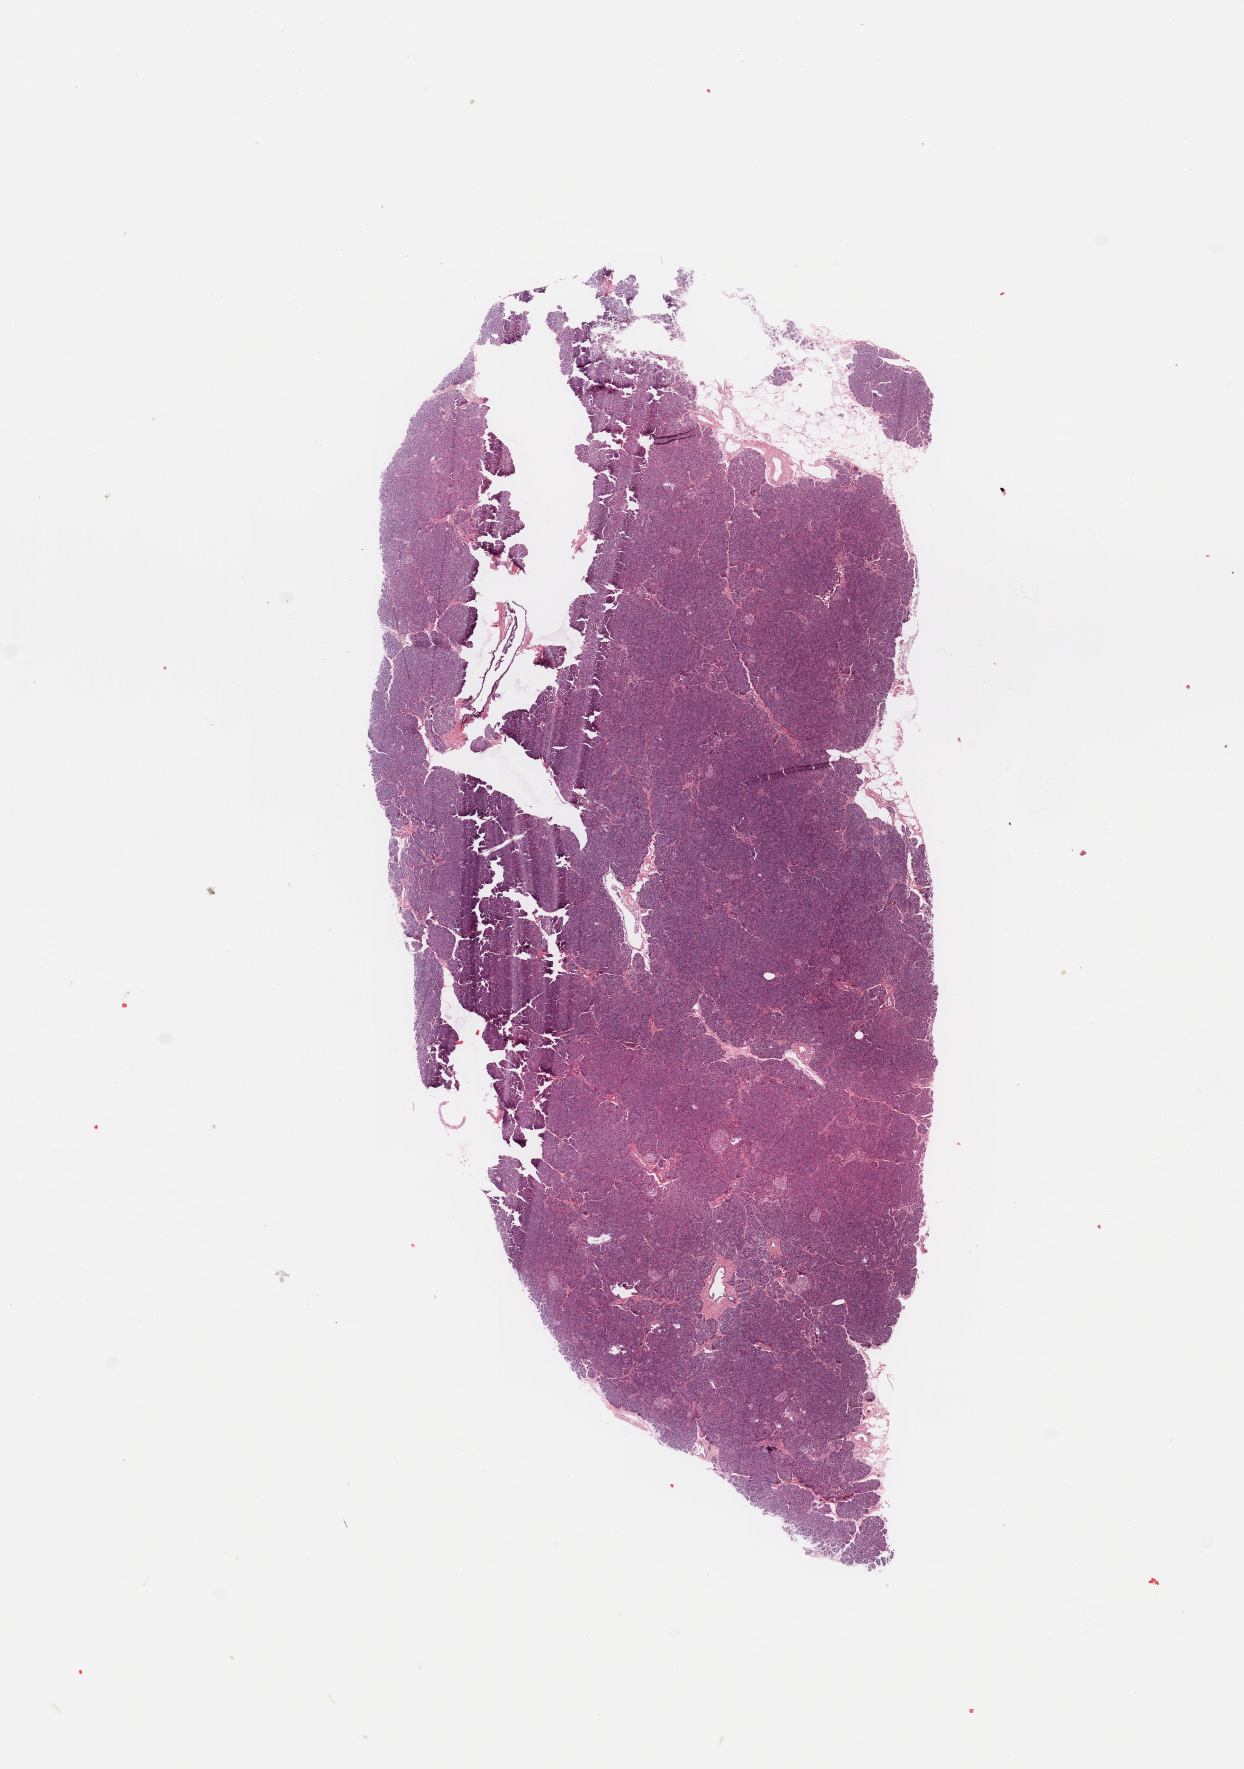
Whole-slide histology image, H&E, a low-resolution overview of the entire scanned area, about 9.8 x 14.0 mm (from a 20x scan), normal (non-tumour) tissue sample, sampled site: pancreas. Male, 54 y/o.
This section: normal (non-tumour) tissue from the same patient. Patient diagnosis: Infiltrating duct carcinoma, NOS.